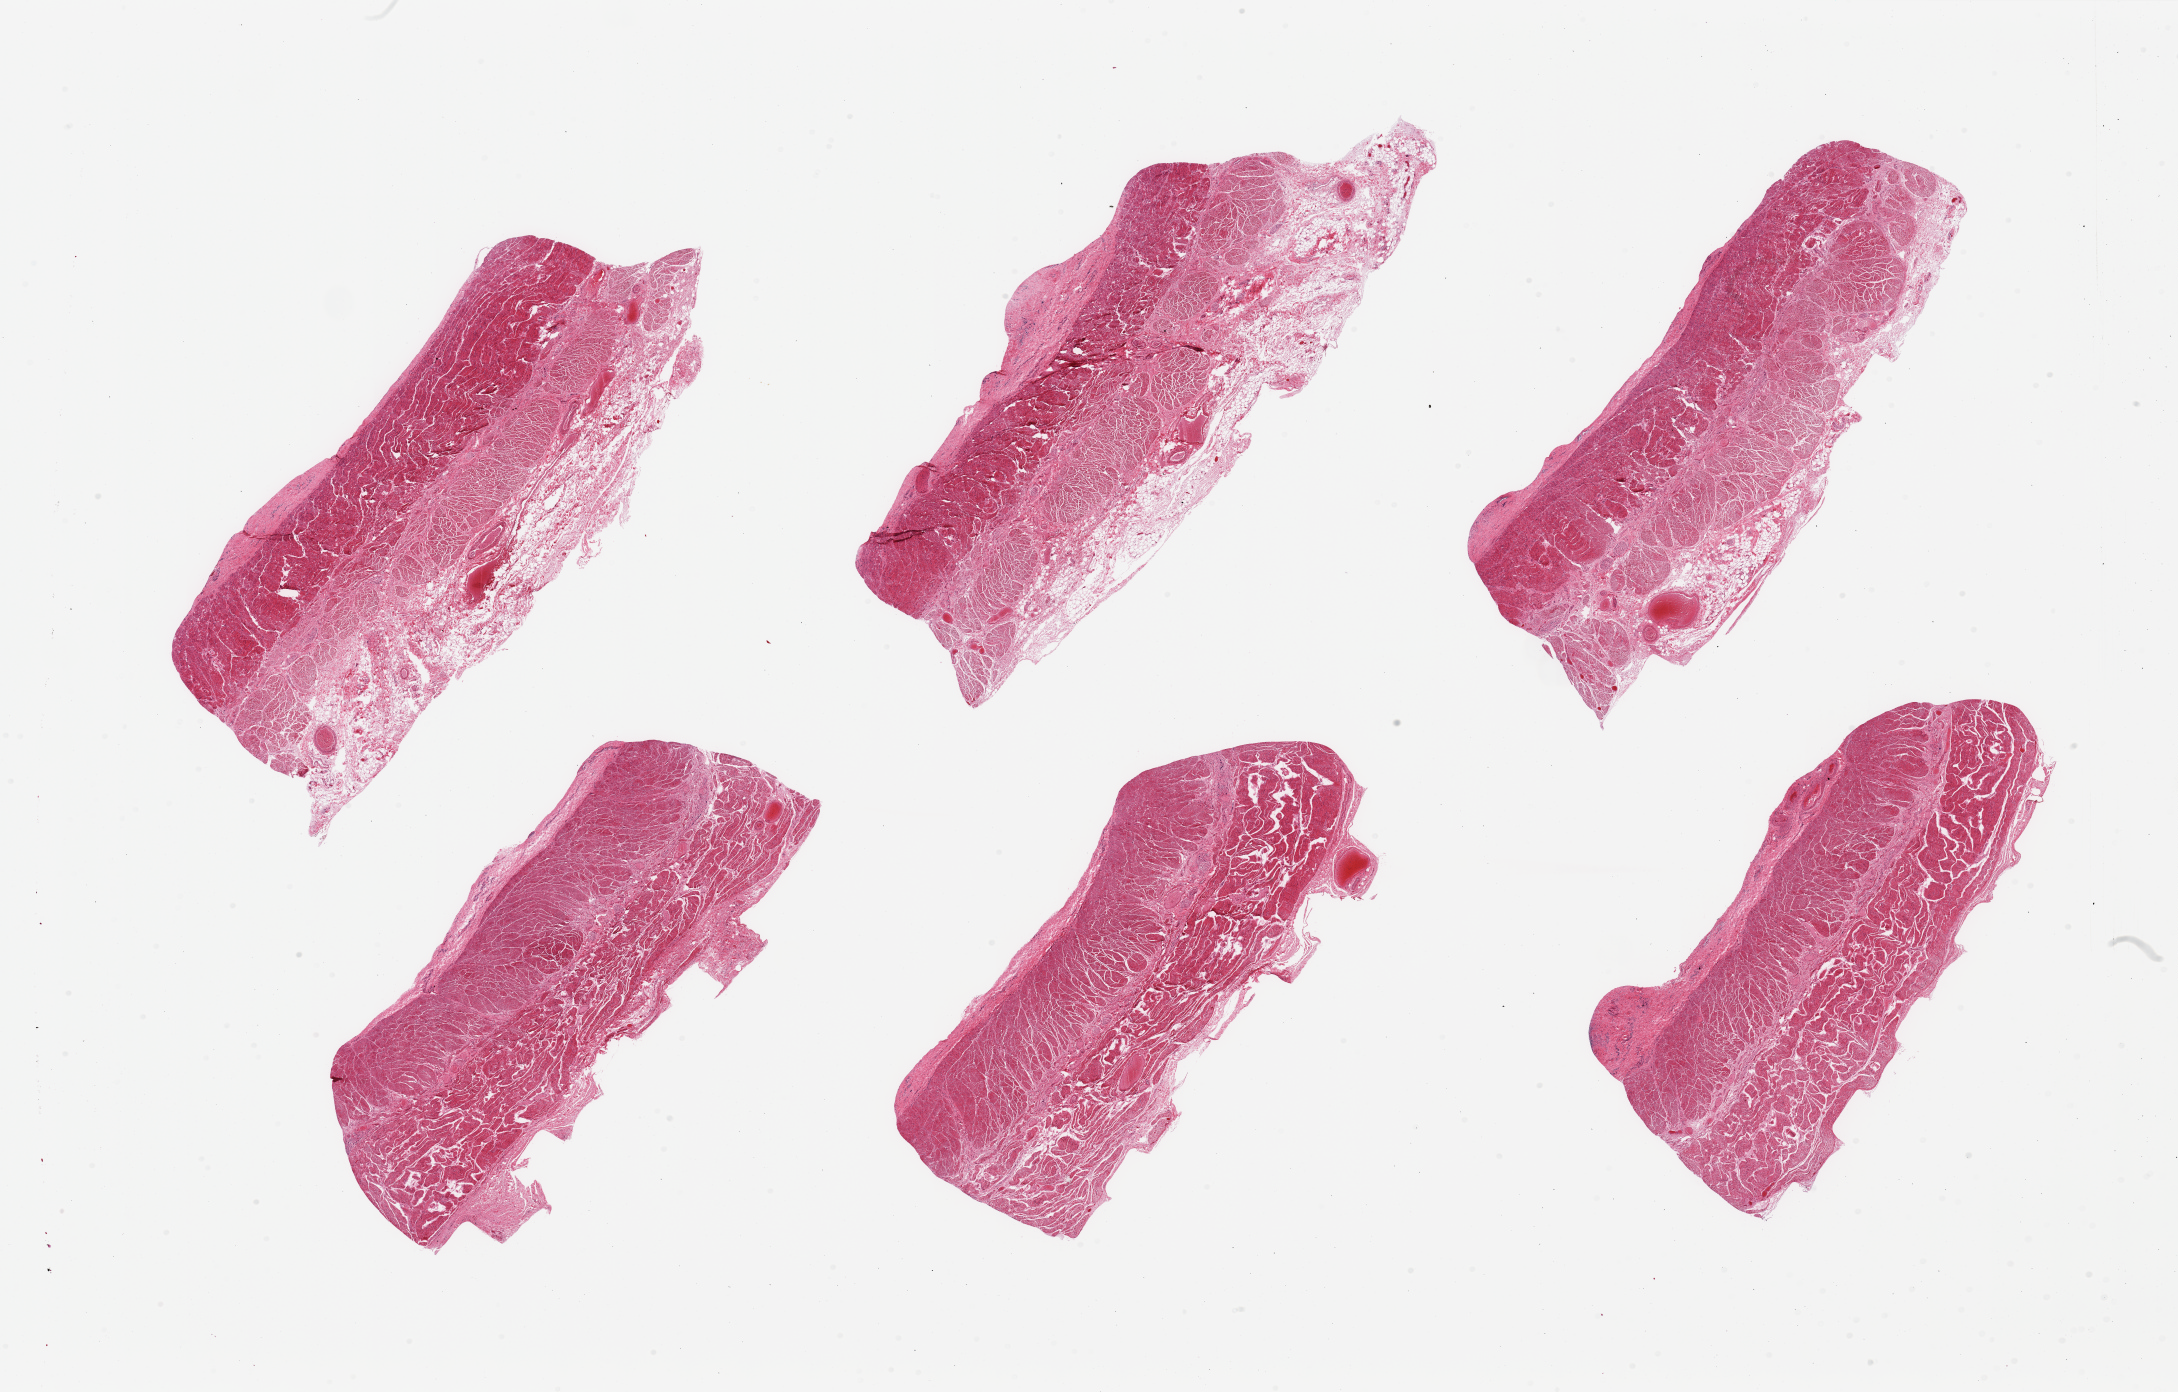
Whole-slide image, H&E stain — whole scanned area (about 34.5 x 22.0 mm) shown as a low-resolution overview, PAXgene-fixed paraffin-embedded (PFPE) section, sampled site (target tissue): gastroesophageal junction, donor tissue sample. Male donor.
Reviewer comment on this tissue sample: 6 pieces; 3 with 1mm thick fatty adventitia.